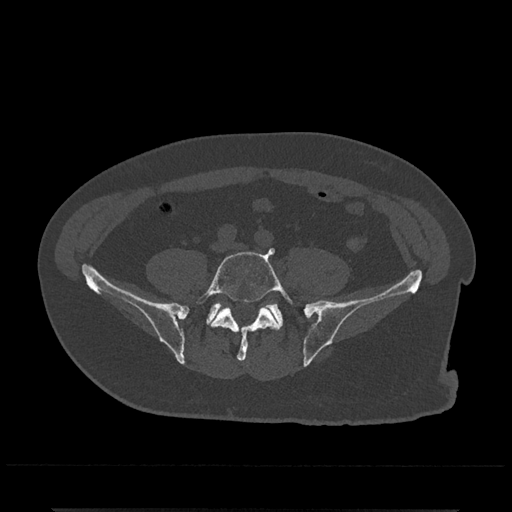
CT including the spine, one axial slice; slice 77 of 797 in the series (ordered by position); bone window (W 1800 / L 400 HU); 0.5 mm slice thickness; 512 × 512 image matrix, field of view 393 × 393 mm. Patient: male, 67 years. From the clinical record (not read from this slice): primary cancer: prostate.
Annotated regions visible in this slice (semi-automatic segmentation, software-assisted and operator-edited):
- L5 vertebra: bounding box (x1, y1, x2, y2) in pixels: (197, 248, 294, 361)